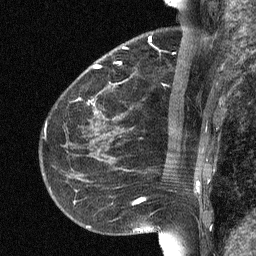
Breast MRI (dynamic contrast-enhanced), one sagittal slice. Slice 23 of 64 in the series (ordered by position). Dynamic contrast-enhanced study with each time point stored as its own series, time point 2 of 3 at this slice position (early post-contrast, ordered by acquisition time). 1.5 T. TE 4.8 ms, TR 27 ms. 256 × 256 image matrix. Patient: female, 51 years. Case-level facts recorded for this patient, not image findings: setting: breast cancer imaged before/during neoadjuvant chemotherapy; receptor status: HR-positive, HER2-negative.
Annotated regions visible in this slice (semi-automatically segmented with operator editing):
- analysis volume of interest (the breast-tissue region the enhancement analysis was run in; not a lesion): bounding box <72,34,182,118> (left, top, right, bottom; pixels)
- tumour enhancement mask (voxels above the 90 % enhancement threshold inside the analysis volume of interest): <93,65,101,68>